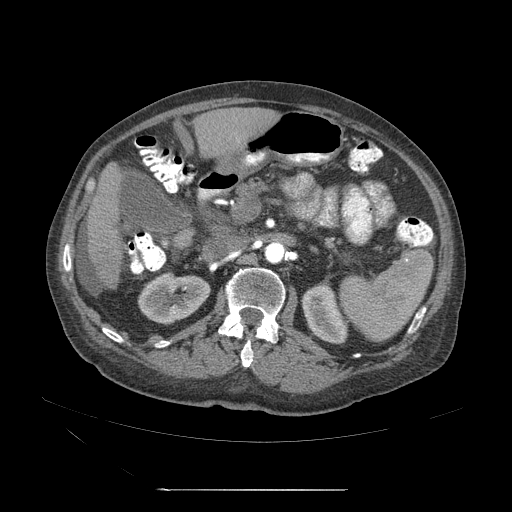
Contrast-enhanced abdominal CT (liver protocol), one axial slice. Position 17 of 71 along the scan axis. Reconstruction kernel STANDARD. Soft-tissue window (W 400 / L 40 HU). 2.5 mm slice thickness. 512 × 512 image matrix, field of view 440 × 440 mm. Case-level facts recorded for this patient, not image findings: diagnosis: hepatocellular carcinoma (patient treated with transarterial chemoembolisation; whether this scan precedes or follows treatment is not stated here); TNM stage (as recorded): Stage-II; Child-Pugh class: A.
Outlined on this slice (semi-automatically segmented with operator editing):
- abdominal aorta: bounding box [x1, y1, x2, y2] px = [265, 243, 286, 266]
- liver parenchyma outside the tumour (the mass and vessels are separate outlines, so this box may not span the whole liver): [91, 178, 131, 284]